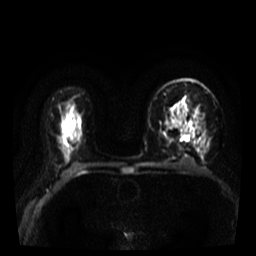
Breast MRI, one axial slice; position 24 of 39 along the scan axis; diffusion-weighted series; image 2 of 4 stored at this slice position (different b-values; order by instance number); 3 T; 5 mm slice thickness; 256 × 256 image matrix, field of view 320 × 320 mm. Female patient.
Structures marked on this image (outlined manually by an expert reader):
- tumour on diffusion-weighted imaging: bounding box <181,129,185,138> (left, top, right, bottom; pixels)